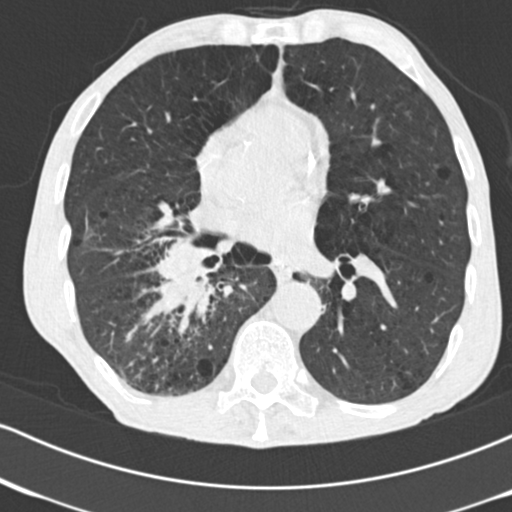
Low-dose screening chest CT, one axial slice. Slice 79 of 182 in the series (ordered by position). Lung window (W 1500 / L -600 HU). 512 × 512 image matrix, field of view 316 × 316 mm.
Annotated regions visible in this slice (manually delineated by an expert):
- lesion 1 (tumor, lower lobe of right lung): bounding box [x1, y1, x2, y2] px = [155, 243, 216, 316]